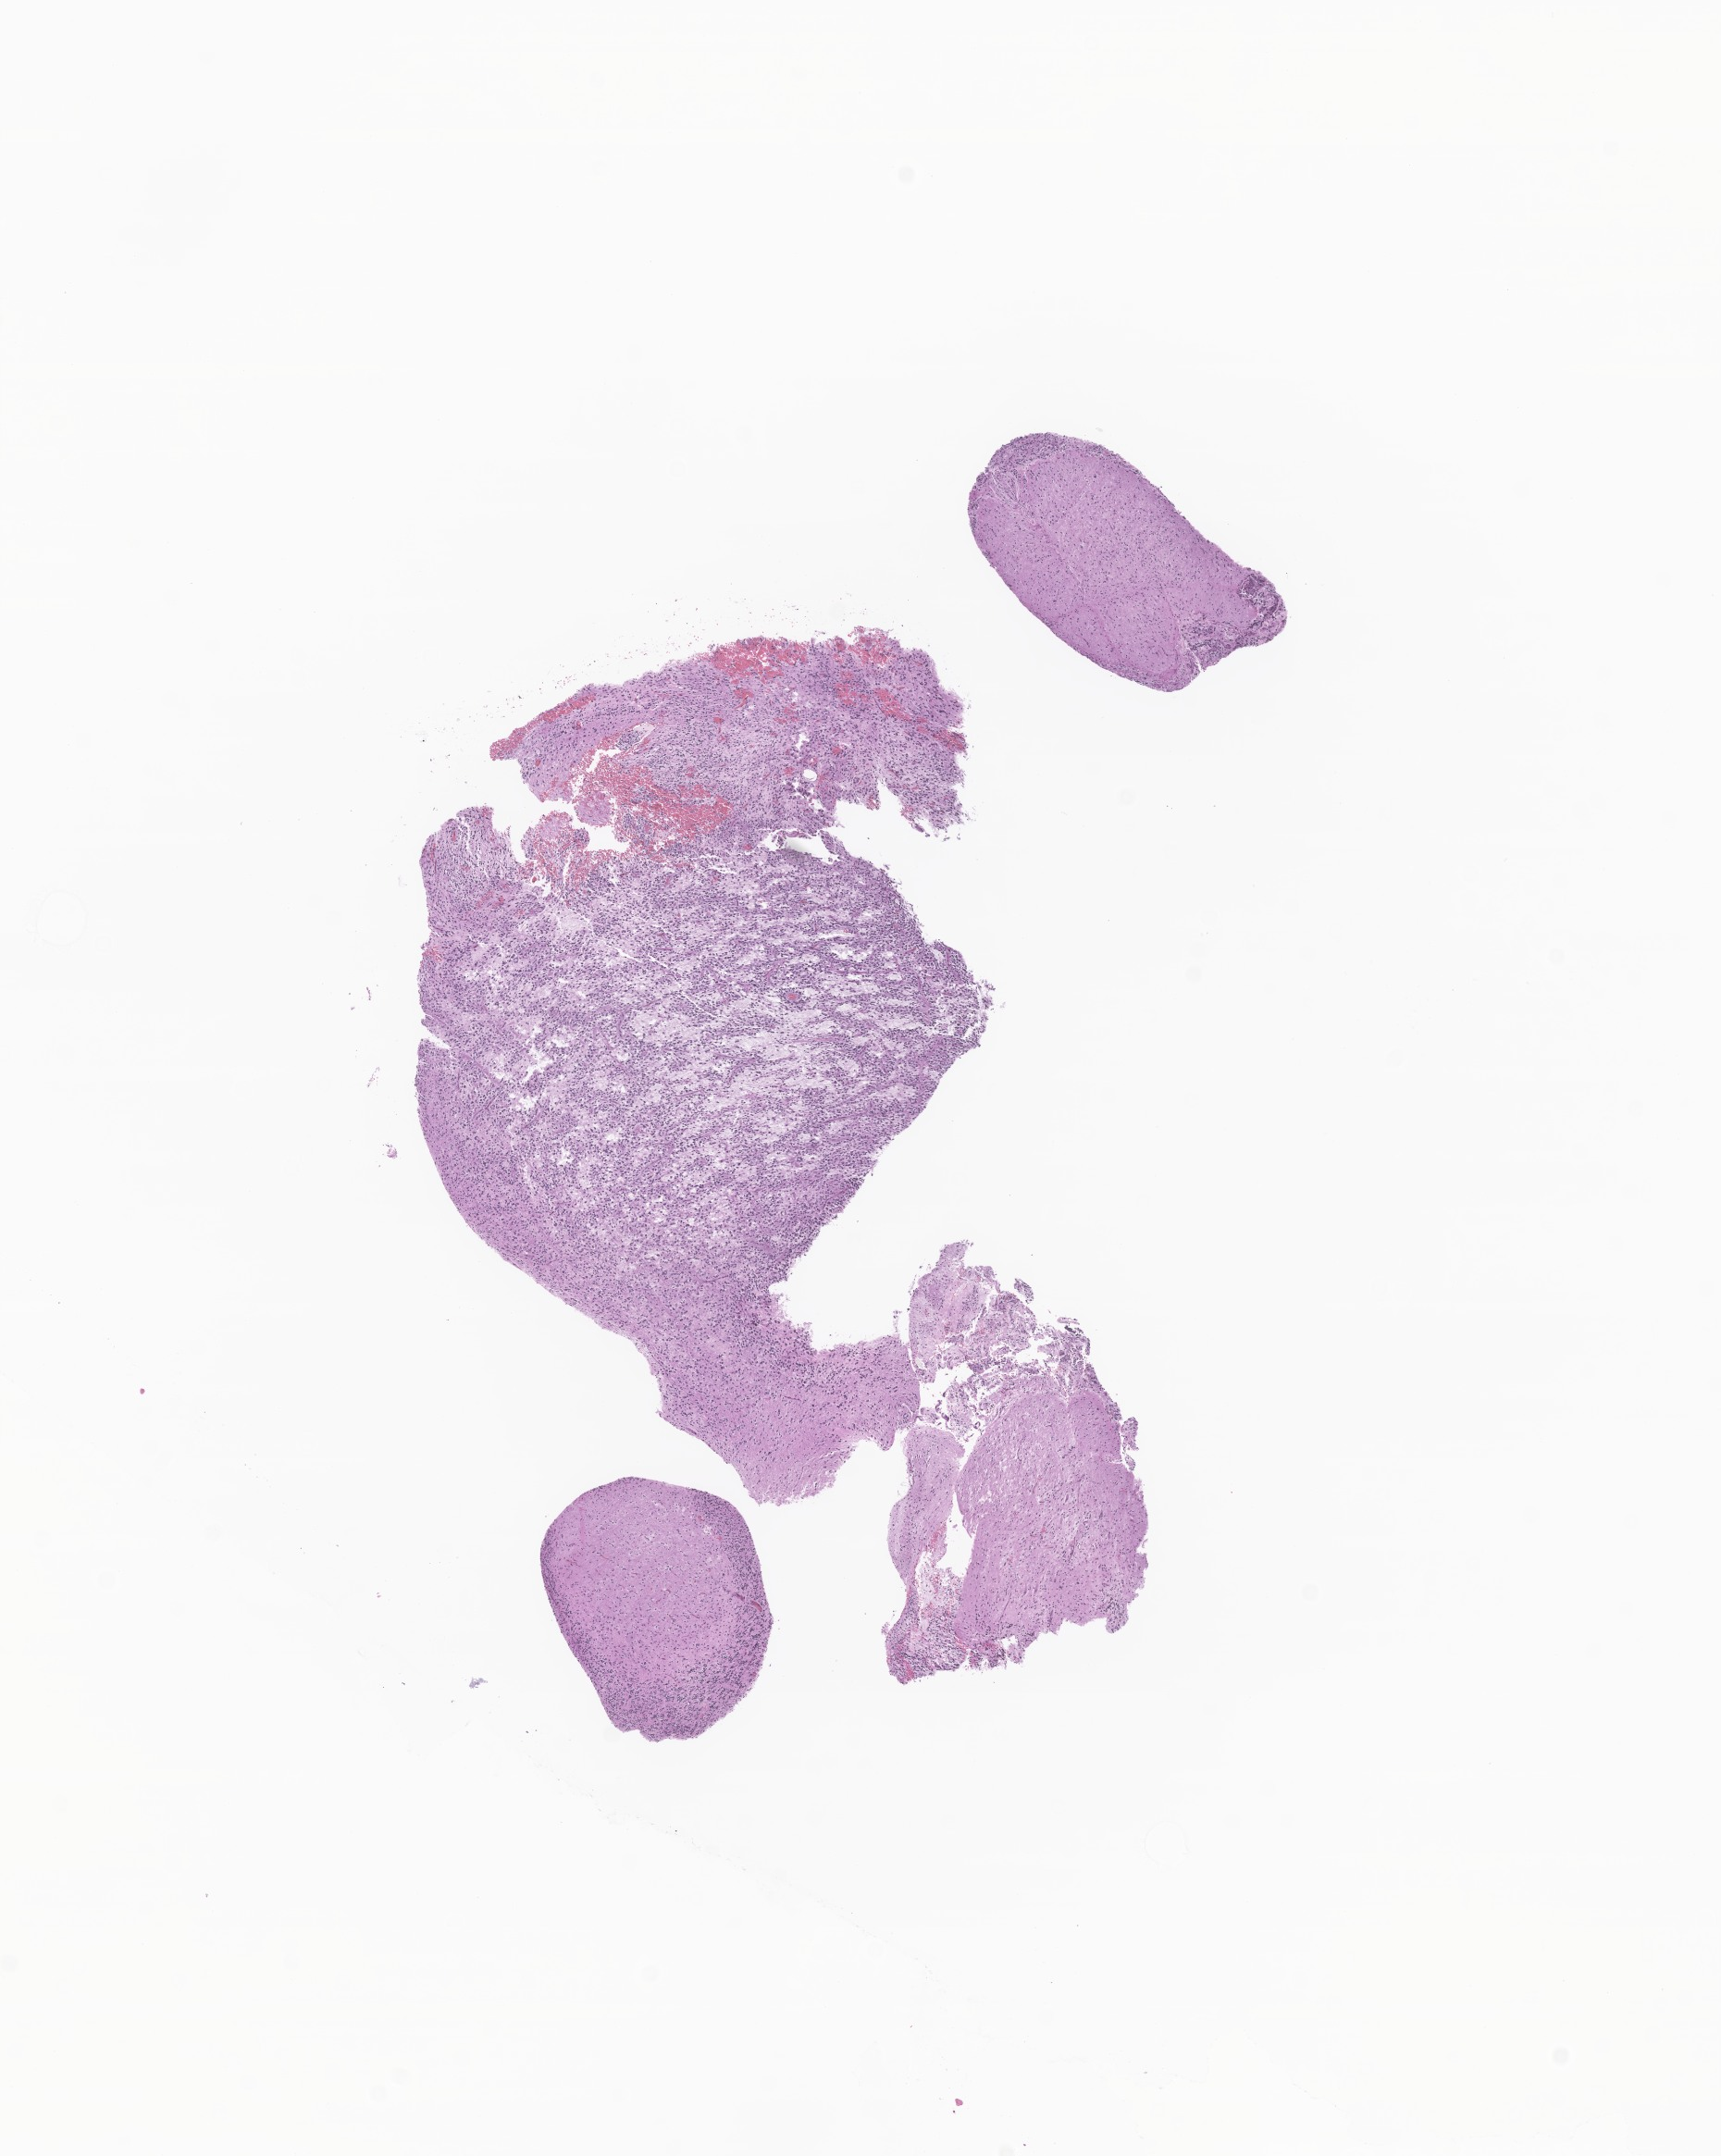
Digitized H&E-stained section of tumor tissue from the brain — low-resolution overview of the scanned area, about 7.8 x 9.8 mm, formalin-fixed paraffin-embedded section. Patient female; age 152 months (12 years 8 months).
* diagnosis: Astrocytoma, NOS